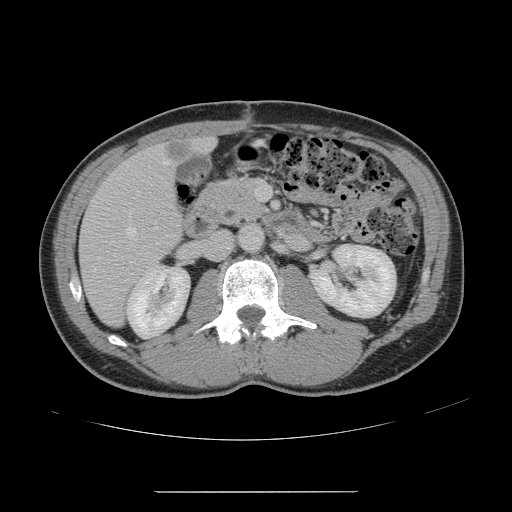
Contrast-enhanced abdominal CT, one axial slice. 120 kVp. Soft-tissue window (W 400 / L 40 HU). 512 × 512 image matrix. Male patient, age 53 years. Case-level facts recorded for this patient, not image findings: diagnosis: colorectal cancer liver metastases, imaged before liver resection; multiple liver metastases: yes; largest metastasis: 2.4 cm; chemotherapy before resection: yes.
Structures marked on this image (outlined manually by an expert reader):
- hepatic veins: bounding box (x1, y1, x2, y2) in pixels: (93, 160, 169, 272)
- liver: (81, 139, 211, 324)
- planned liver remnant (the part of the liver to remain after resection): (199, 140, 212, 151)
- portal vein (with intrahepatic branches): (137, 183, 267, 200)
- liver metastasis: (166, 142, 194, 162)